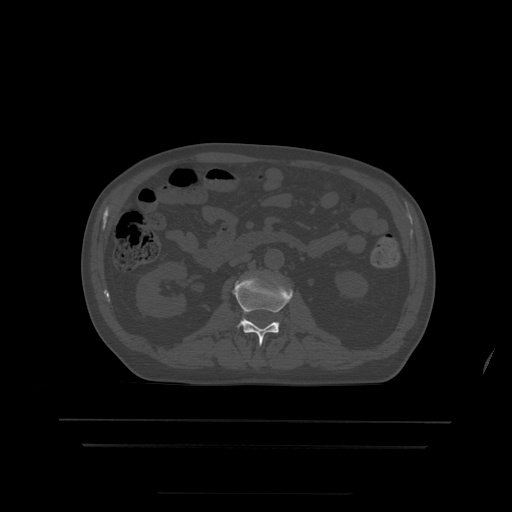
CT including the spine, one axial slice. Position 142 of 522 along the scan axis. Bone window (W 1800 / L 400 HU). 1.25 mm slice thickness. 512 × 512 image matrix, field of view 436 × 436 mm. Patient age 68 years. From the clinical record (not read from this slice): primary cancer: urothelial.
Structures marked on this image (semi-automatically segmented with operator editing):
- L2 vertebra: bounding box <234,276,293,346> (left, top, right, bottom; pixels)